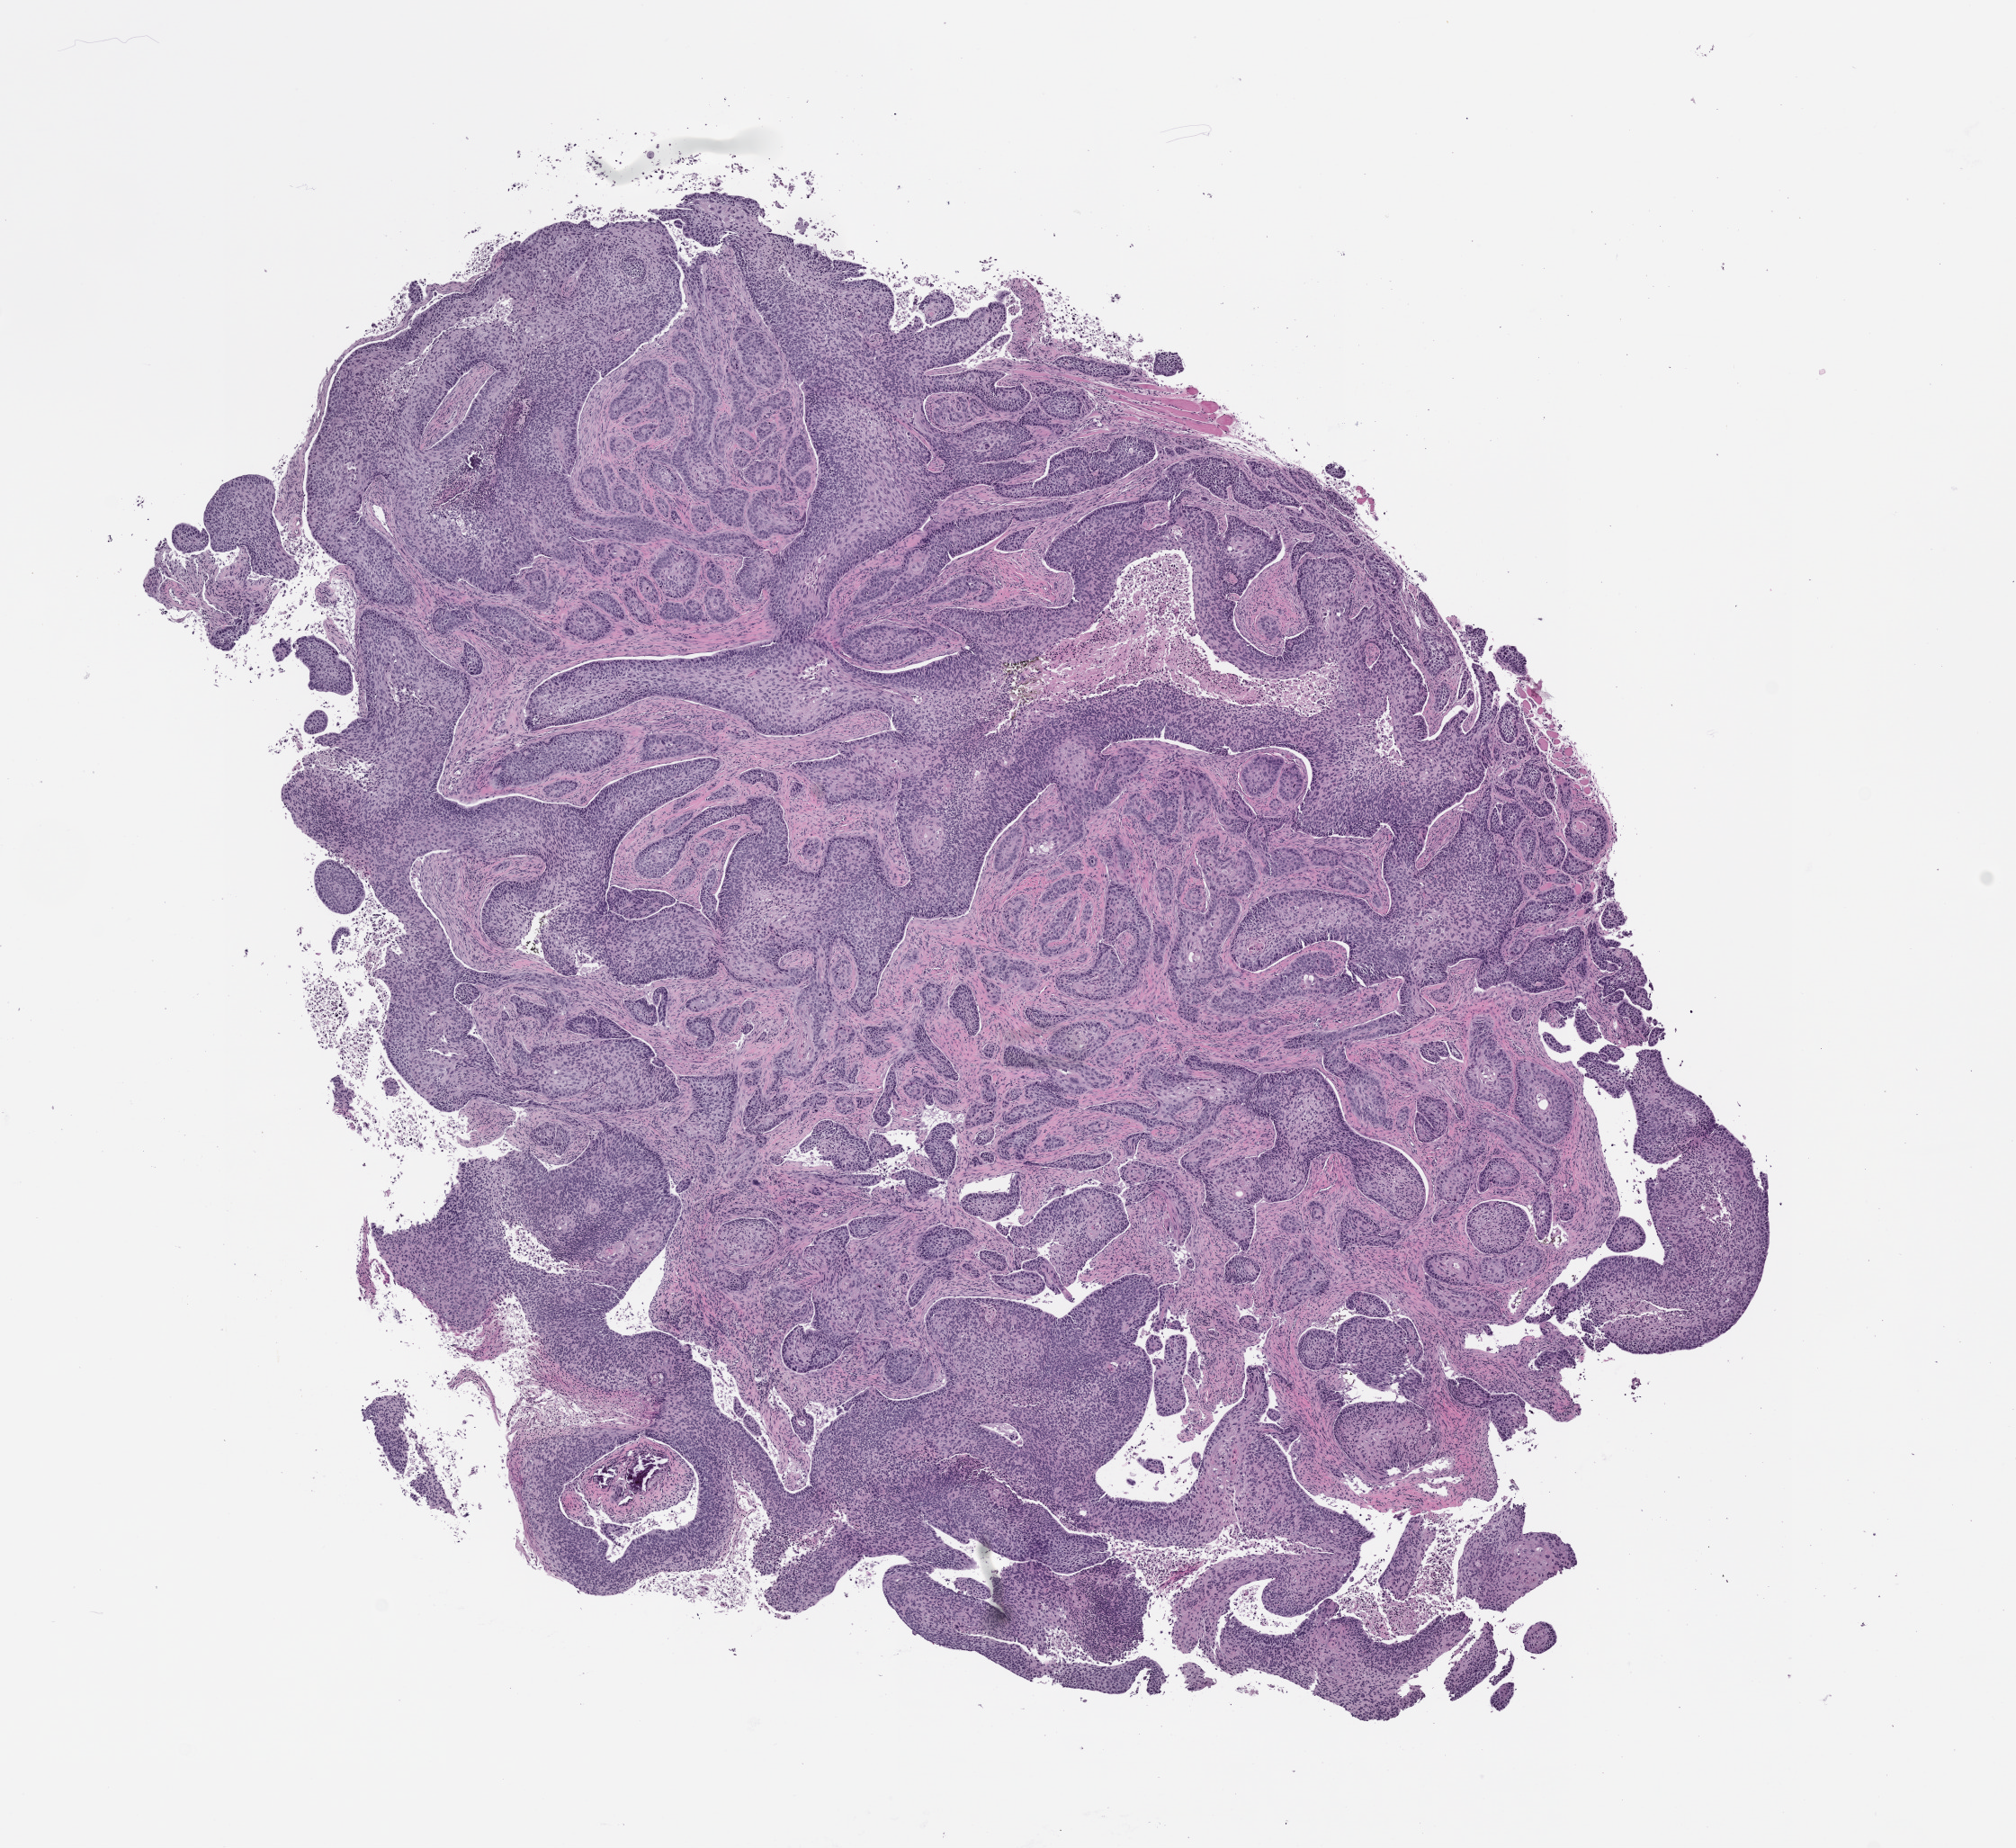
Whole-slide image, hematoxylin and eosin (H&E): patient-derived xenograft (human tumor grown in a mouse), passage 1 — shown as a low-resolution overview of the whole scanned area (about 9.0 x 8.3 mm). Formalin-fixed, paraffin-embedded (FFPE) tissue. Originating tumor site category: head and neck.
Originating patient diagnosis: Head and Neck Squamous Cell Carcinoma.